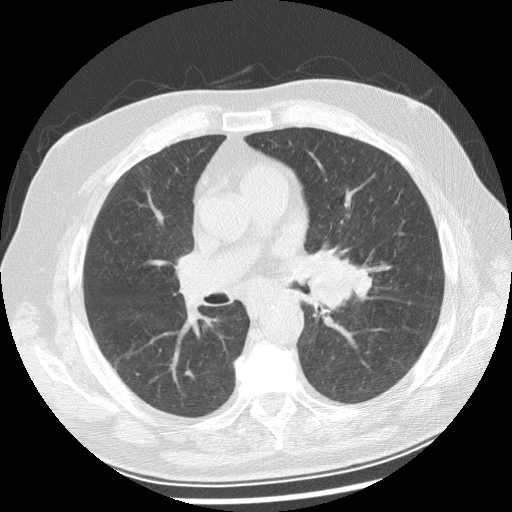
Low-dose screening chest CT, axial slice; baseline annual screen; lung window (W 1500 / L -600 HU); slice 111 of 250 in the series; 512 × 512 image matrix. Male, age 70 years at enrolment.
• Expert reader's lesion annotation, bounding box (x1, y1, x2, y2) in pixels: (286, 241, 369, 315).
• No non-calcified nodule or mass ≥4 mm was recorded by the screening reader at this exam.
• Participant outcome: lung cancer diagnosed 29 days after this screen — squamous cell carcinoma, keratinizing, NOS, left main stem bronchus, moderately differentiated (G2), stage IIIB (AJCC 6th edition), 40 mm at pathology.